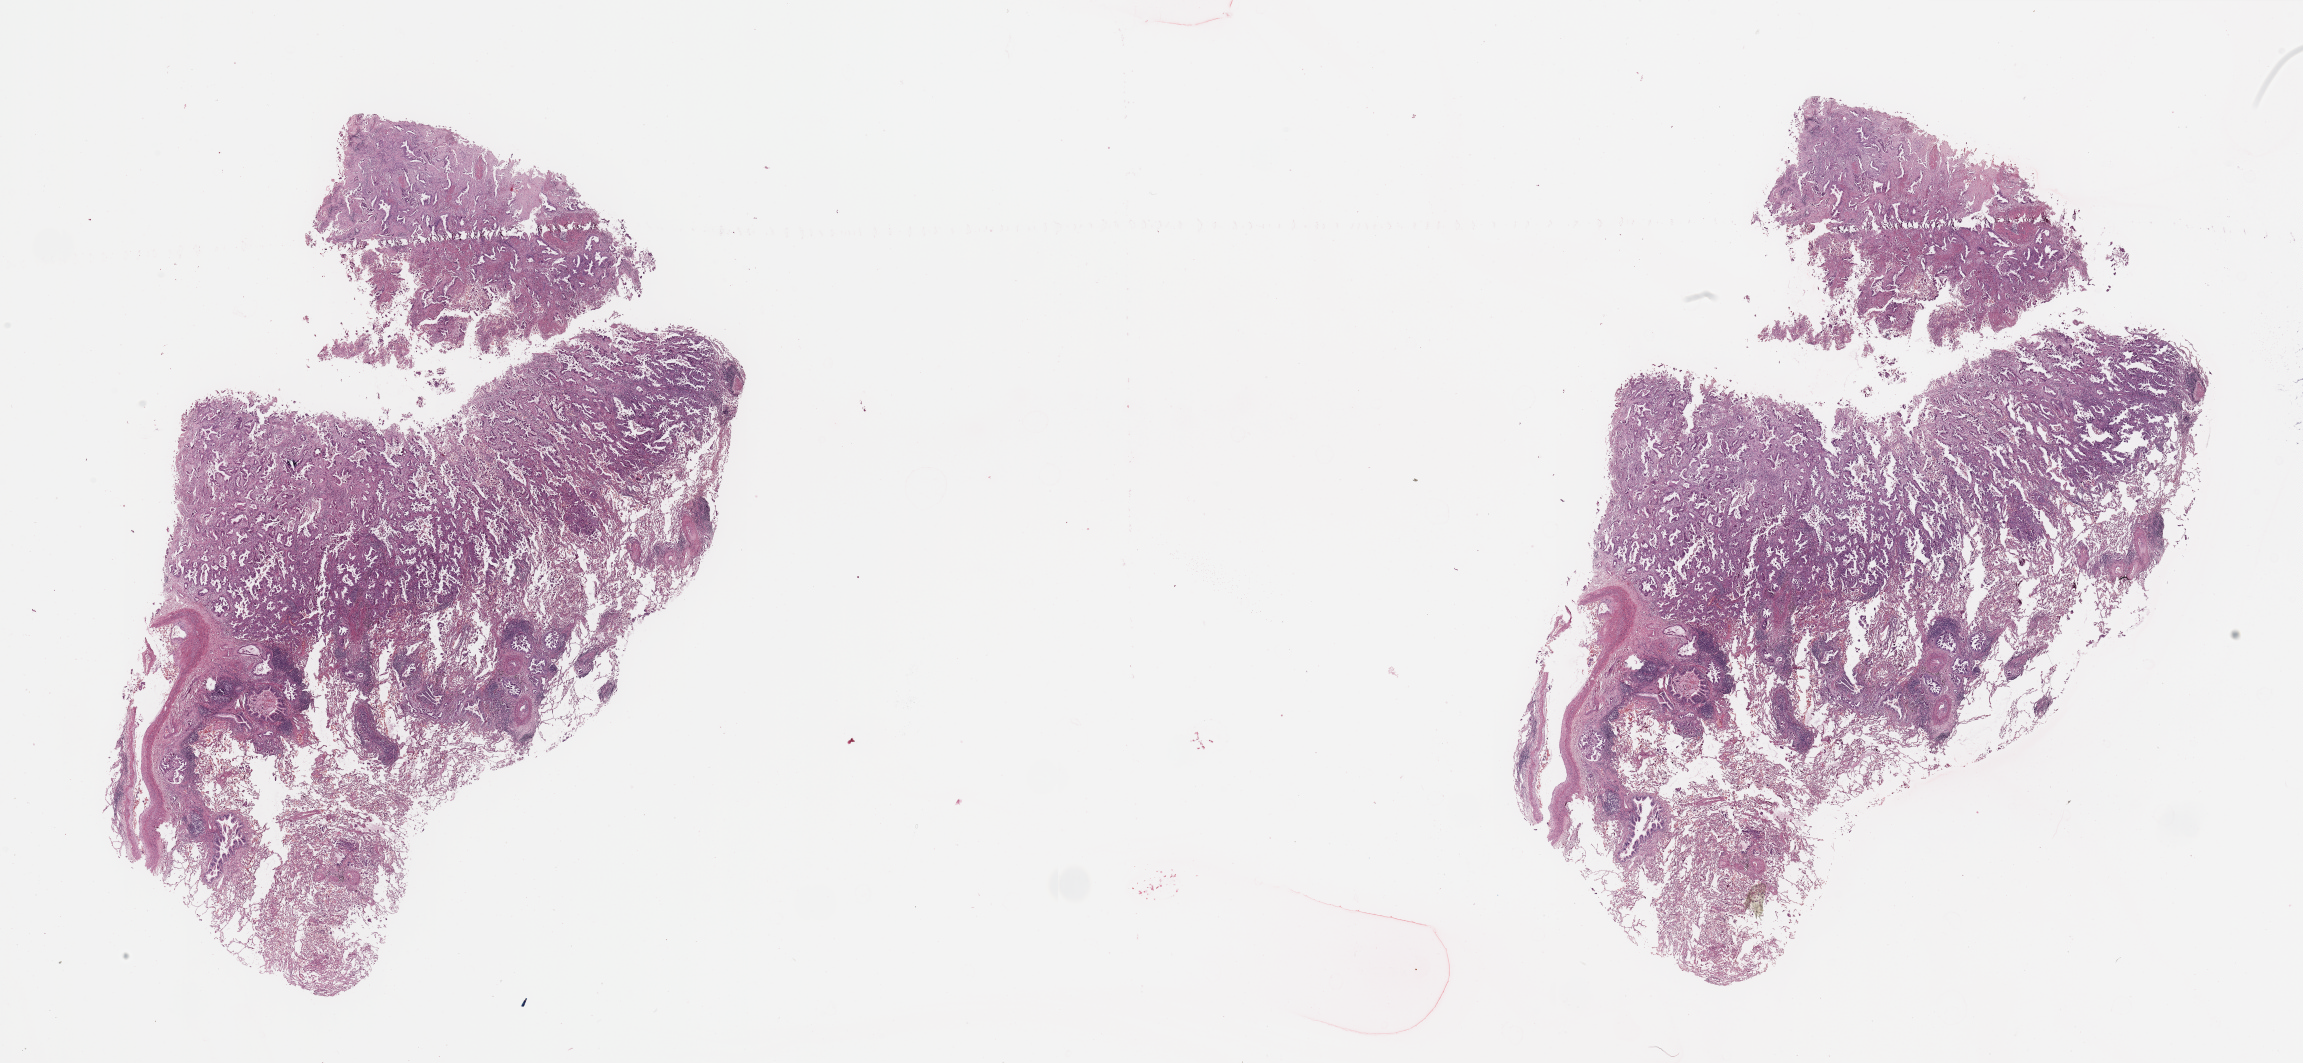
Whole-slide histology image, H&E — low-resolution overview of the scanned area, about 36.4 x 16.8 mm (acquisition: 20x scan); tumour tissue sample, lung. Patient: female, age 73 years. Histologic grade: G2 (moderately differentiated).
AJCC pathologic stage: IIIA. Histologic diagnosis: Adenocarcinoma, NOS.